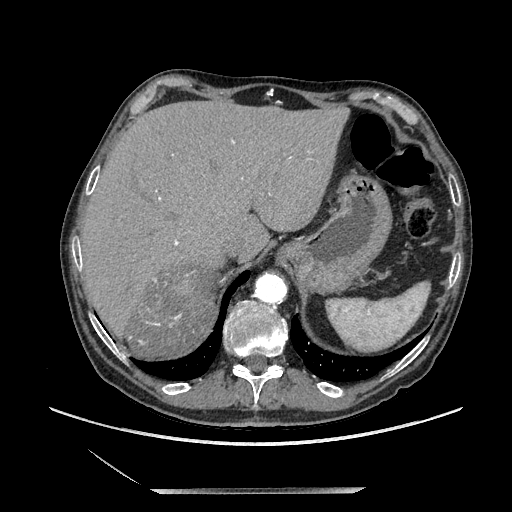
Contrast-enhanced abdominal CT, one axial slice. Position 169 of 243 along the scan axis. Soft-tissue window (W 400 / L 40 HU). 512 × 512 image matrix, field of view 420 × 420 mm. Male patient. Case-level facts recorded for this patient, not image findings: diagnosis: adrenocortical carcinoma; tumour side: right adrenal; tumour size at pathology: 16 cm; Ki-67 index: 17 %.
Outlined on this slice (semi-automatically segmented with operator editing):
- mass: bounding box <125,270,216,358> (left, top, right, bottom; pixels)